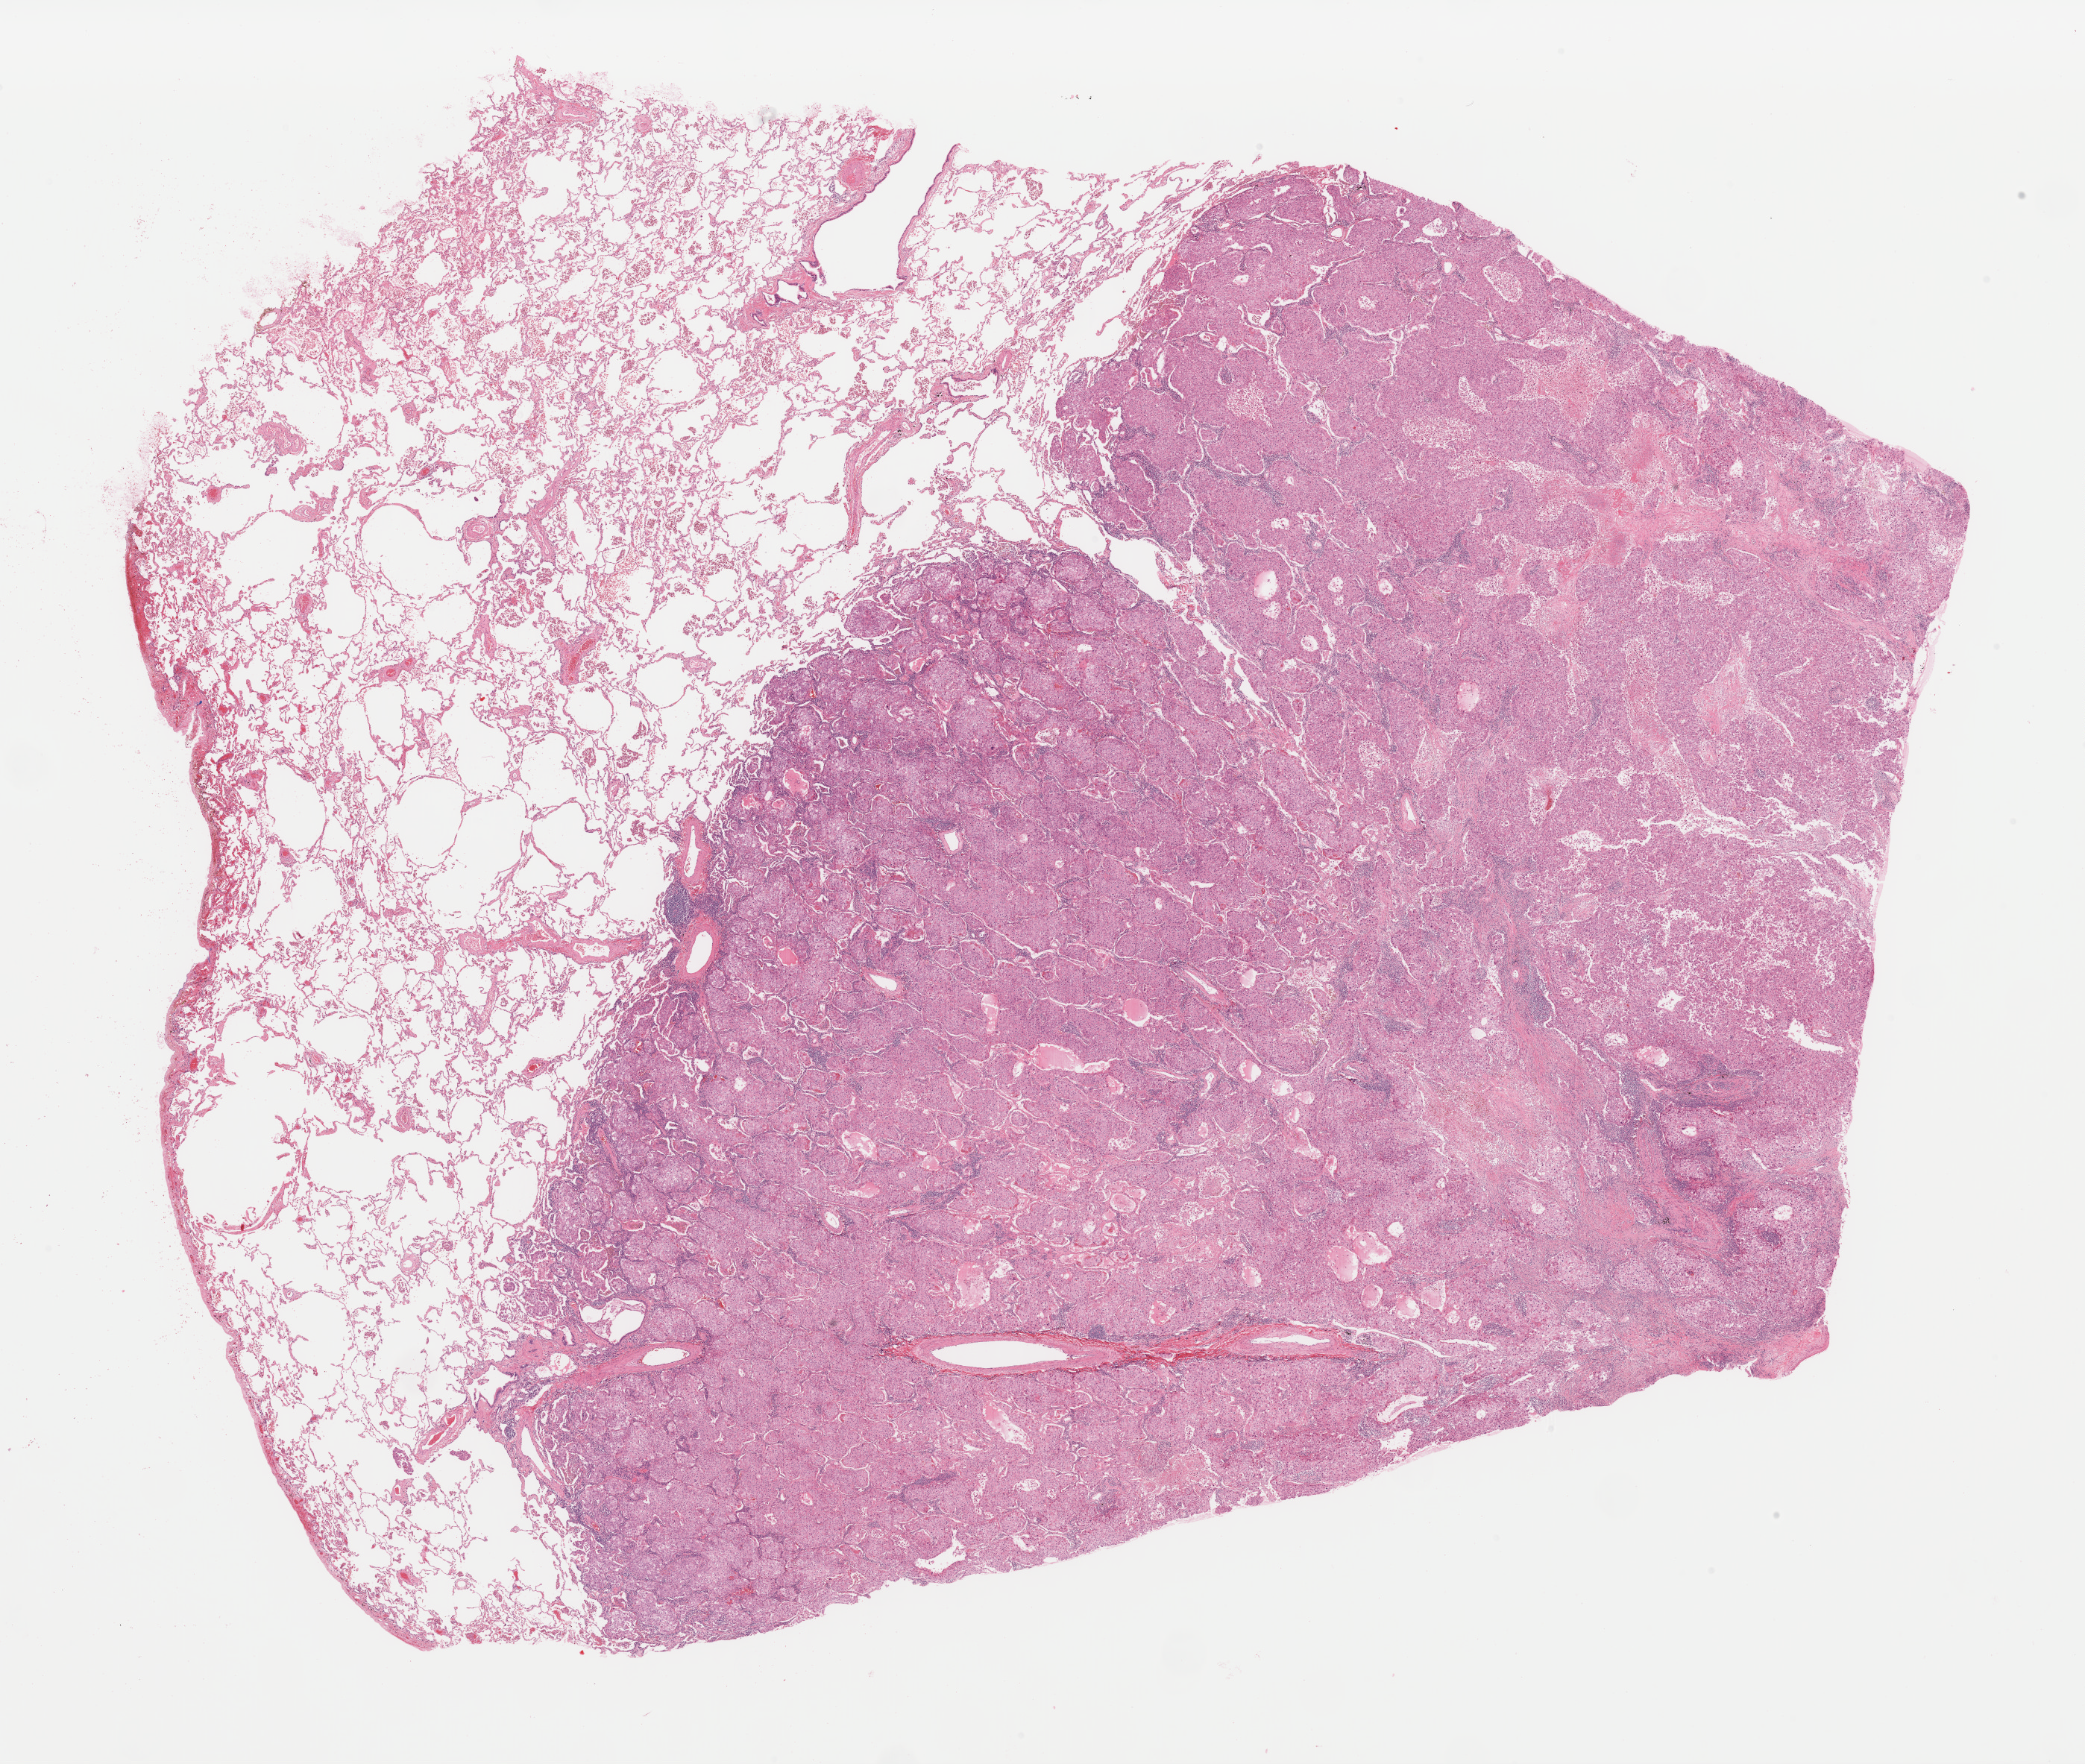
Whole-slide histology image, Hematoxylin and eosin (H&E) stained — shown as a low-resolution overview of the whole scanned area (about 22.1 x 18.7 mm, acquisition: 40x scan), FFPE section, lung, primary tumour sample. Patient: female, age at initial diagnosis 60 years.
- AJCC pathologic stage: IIB (7th edition)
- diagnosis: Adenocarcinoma with mixed subtypes (upper lobe, lung)
- laterality: right